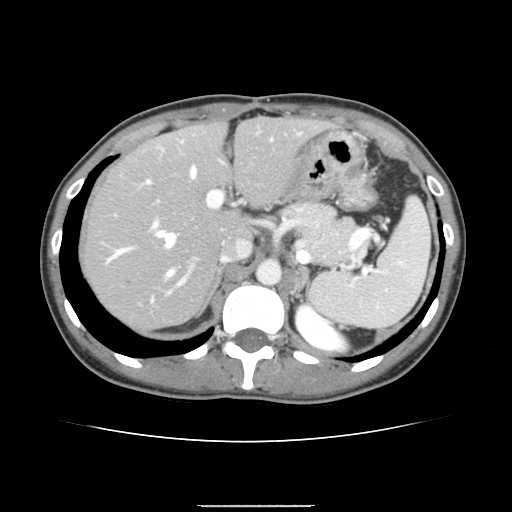
Contrast-enhanced abdominal CT, one axial slice; position 102 of 150 along the scan axis; 120 kVp; intravenous contrast given; soft-tissue window (W 400 / L 40 HU); 2.5 mm slice thickness; 512 × 512 image matrix, field of view 324 × 324 mm. Female patient, age 32 years. Case-level facts recorded for this patient, not image findings: diagnosis: colorectal cancer liver metastases, imaged before liver resection; multiple liver metastases: yes.
Outlined on this slice (expert manual segmentation):
- hepatic veins: box from (x=109, y=167) to (x=196, y=276) px
- liver: (x=84, y=116)–(x=323, y=330)
- planned liver remnant (the part of the liver to remain after resection): (x=83, y=116)–(x=320, y=281)
- portal vein (with intrahepatic branches): (x=106, y=133)–(x=300, y=293)
- liver metastasis: (x=126, y=279)–(x=132, y=286)